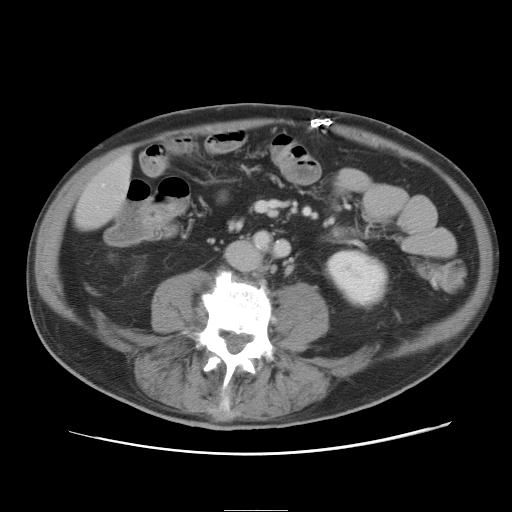
Contrast-enhanced abdominal CT, one axial slice; slice 2 of 89 in the series (ordered by position); 120 kVp; soft-tissue window (W 400 / L 40 HU); 5 mm slice thickness; 512 × 512 image matrix. Male patient, age 69 years. Case-level facts recorded for this patient, not image findings: diagnosis: colorectal cancer liver metastases, imaged before liver resection; multiple liver metastases: no.
Annotated regions visible in this slice (outlined manually by an expert reader):
- liver: bounding box <76,158,132,230> (left, top, right, bottom; pixels)
- planned liver remnant (the part of the liver to remain after resection): <76,159,132,230>